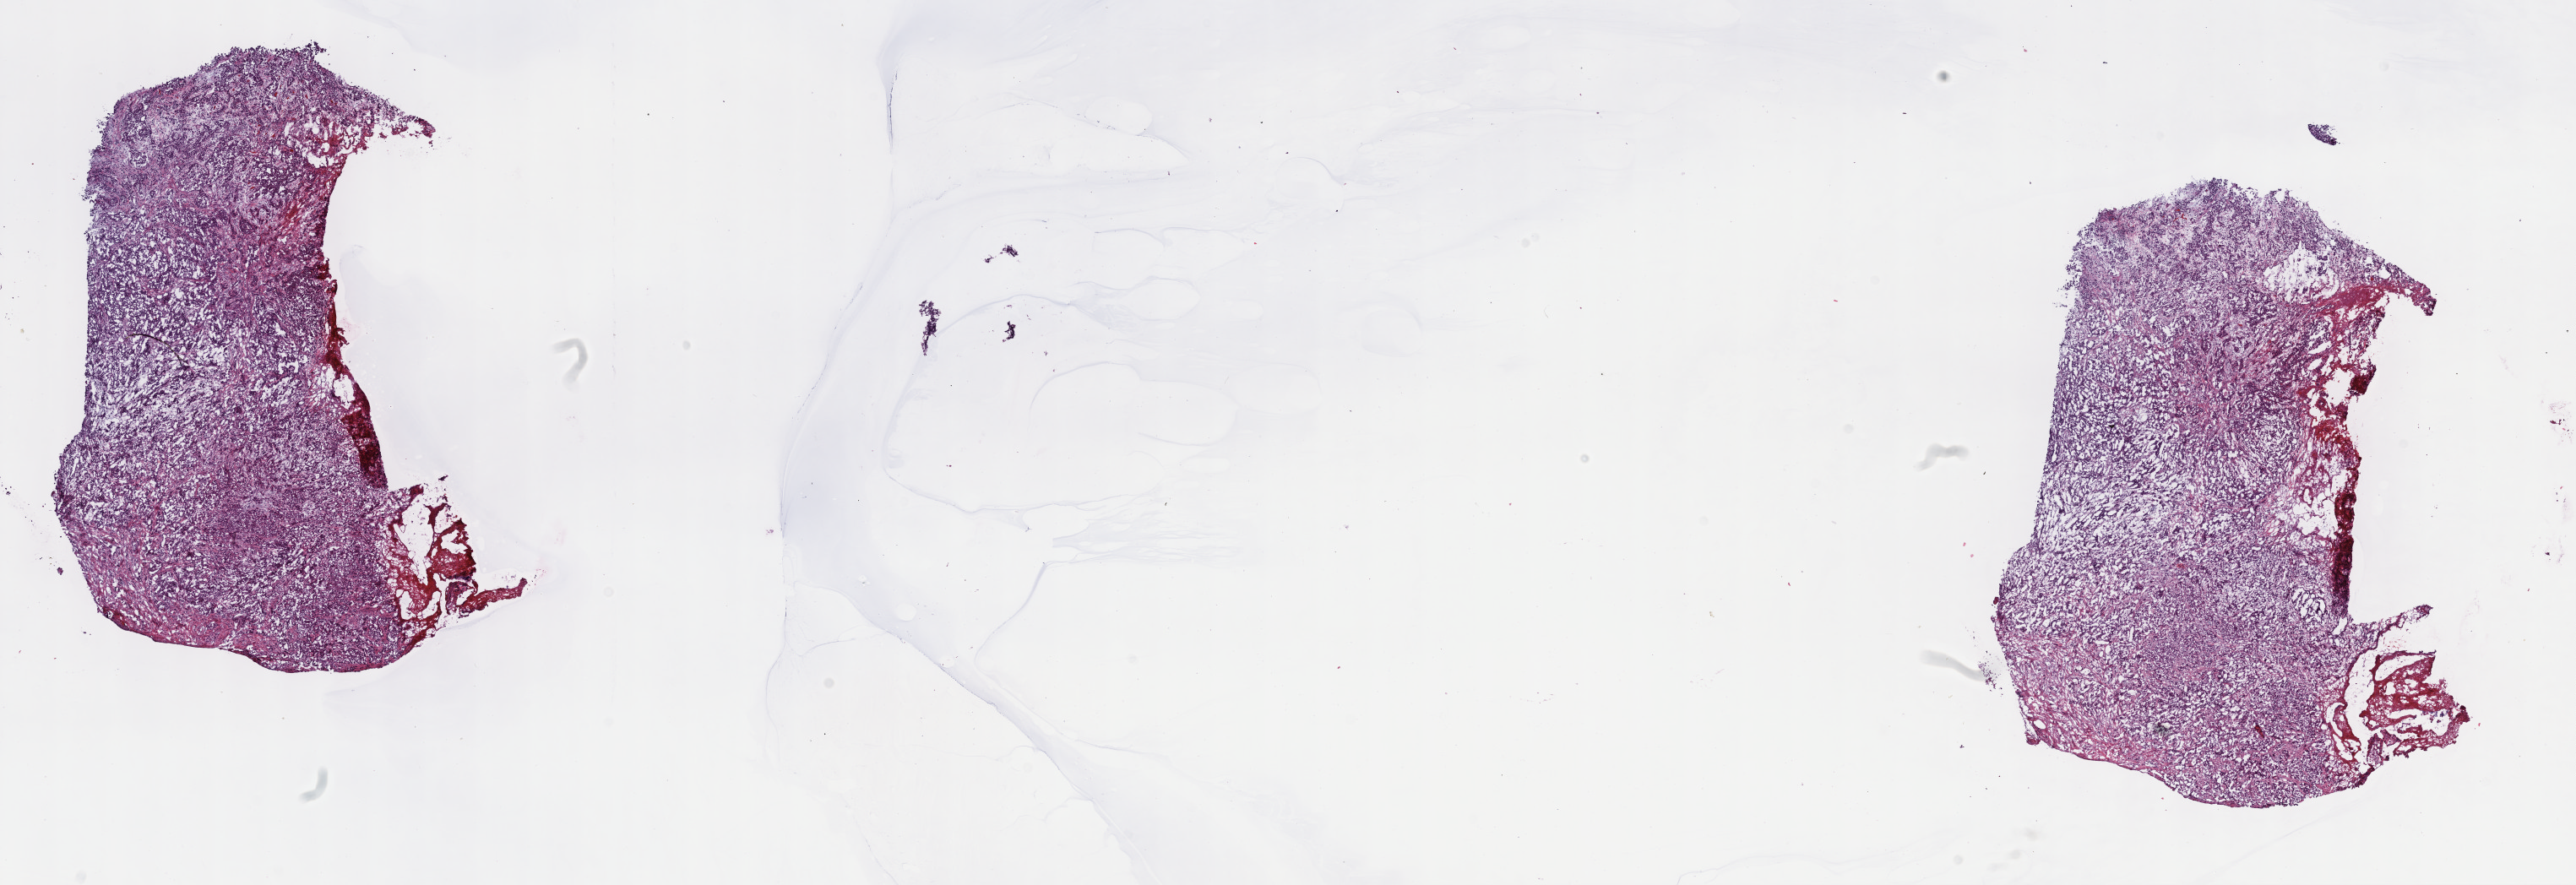
Hematoxylin and eosin (H&E) stained whole-slide image — a low-resolution overview of the entire scanned area, about 24.7 x 8.5 mm (from a 40x scan); frozen section; mesothelium, primary tumour sample. Patient: male, age at initial diagnosis 66 years. Slide review estimates, as recorded: tumour cells 100%, tumour nuclei 75%, normal cells 0%, stromal cells 0%, necrosis 0%. Infiltration values recorded for this section: lymphocyte infiltration 3%, monocyte infiltration 0%, neutrophil infiltration 0%.
• TNM: T1 N0 M0
• histologic diagnosis: Epithelioid mesothelioma, malignant (pleura, NOS)
• AJCC pathologic stage: I